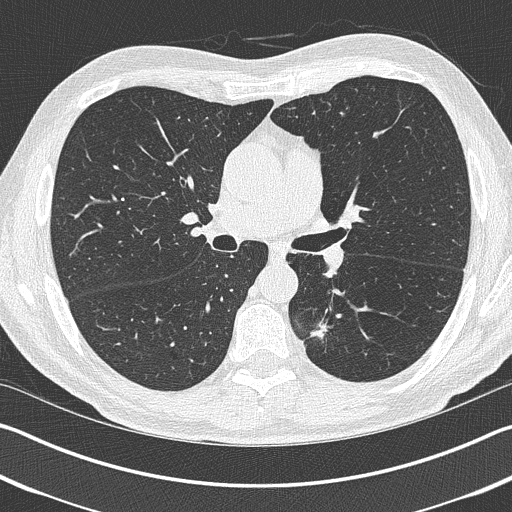
Low-dose screening chest CT, axial slice. First (baseline) screen. Lung window (W 1500 / L -600 HU). Lung (sharp) reconstruction kernel (B50f). Male participant, aged 69 years at enrolment.
Lesion marked by an expert reader, bounding box <301,308,356,360> (left, top, right, bottom; pixels). Reader record for this screening exam (exam-level; its link to the box is not recorded): non-calcified nodule or mass ≥4 mm, left upper lobe, 19 × 19 mm, spiculated (stellate) margins, pre-existing on the prior screen: yes. Official screen result: positive, change unspecified: nodule(s) >= 4 mm or enlarging nodule(s), mass(es), or other non-specific abnormalities suspicious for lung cancer. Participant outcome: lung cancer diagnosed 202 days after this screen — non-small cell carcinoma, left lower lobe, stage IIIA (AJCC 6th edition), 20 mm at pathology.